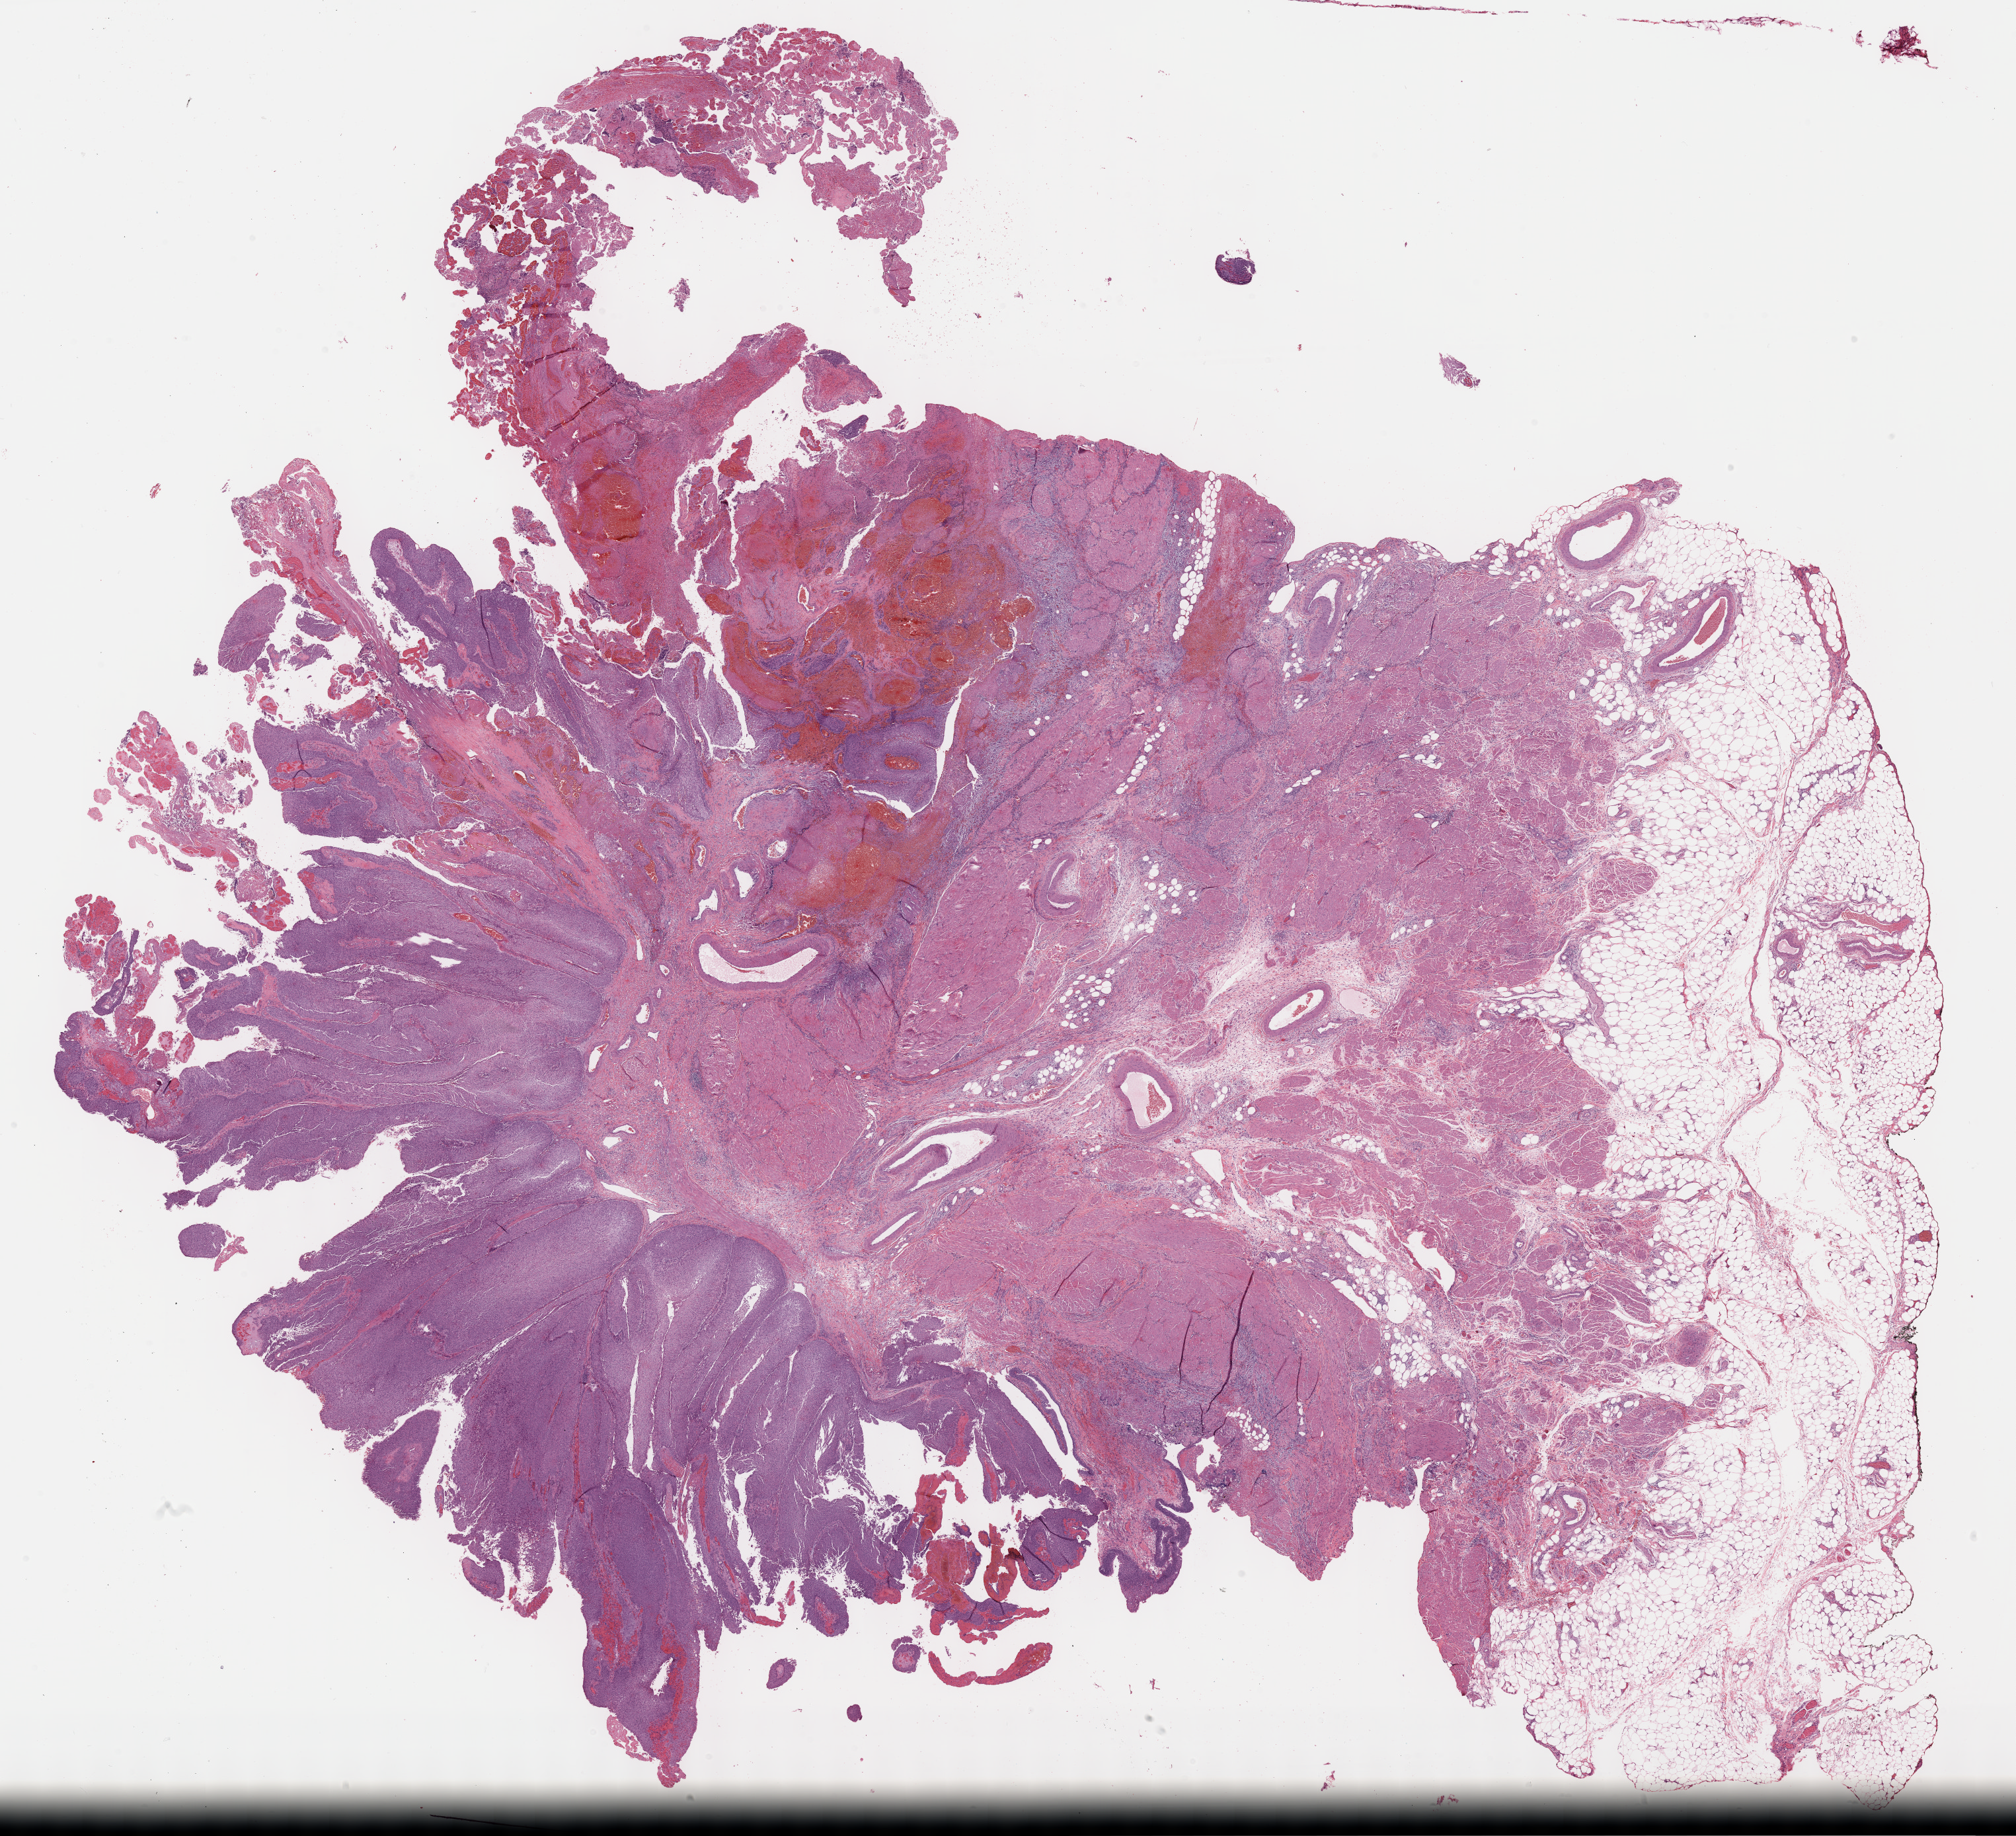
Whole-slide histology image, H&E-stained — shown as a low-resolution overview of the whole scanned area (about 24.7 x 22.5 mm, slide scanned at 40x), formalin-fixed paraffin-embedded (FFPE) diagnostic section, sample: primary tumour, bladder. Patient: male, age at initial diagnosis 61 years. Histologic grade: high grade.
* histologic diagnosis: Transitional cell carcinoma (lateral wall of bladder)
* AJCC pathologic stage: II (6th edition)
* lymph nodes positive (case pathology): 0 of 16 examined
* TNM: T2b N0 M0